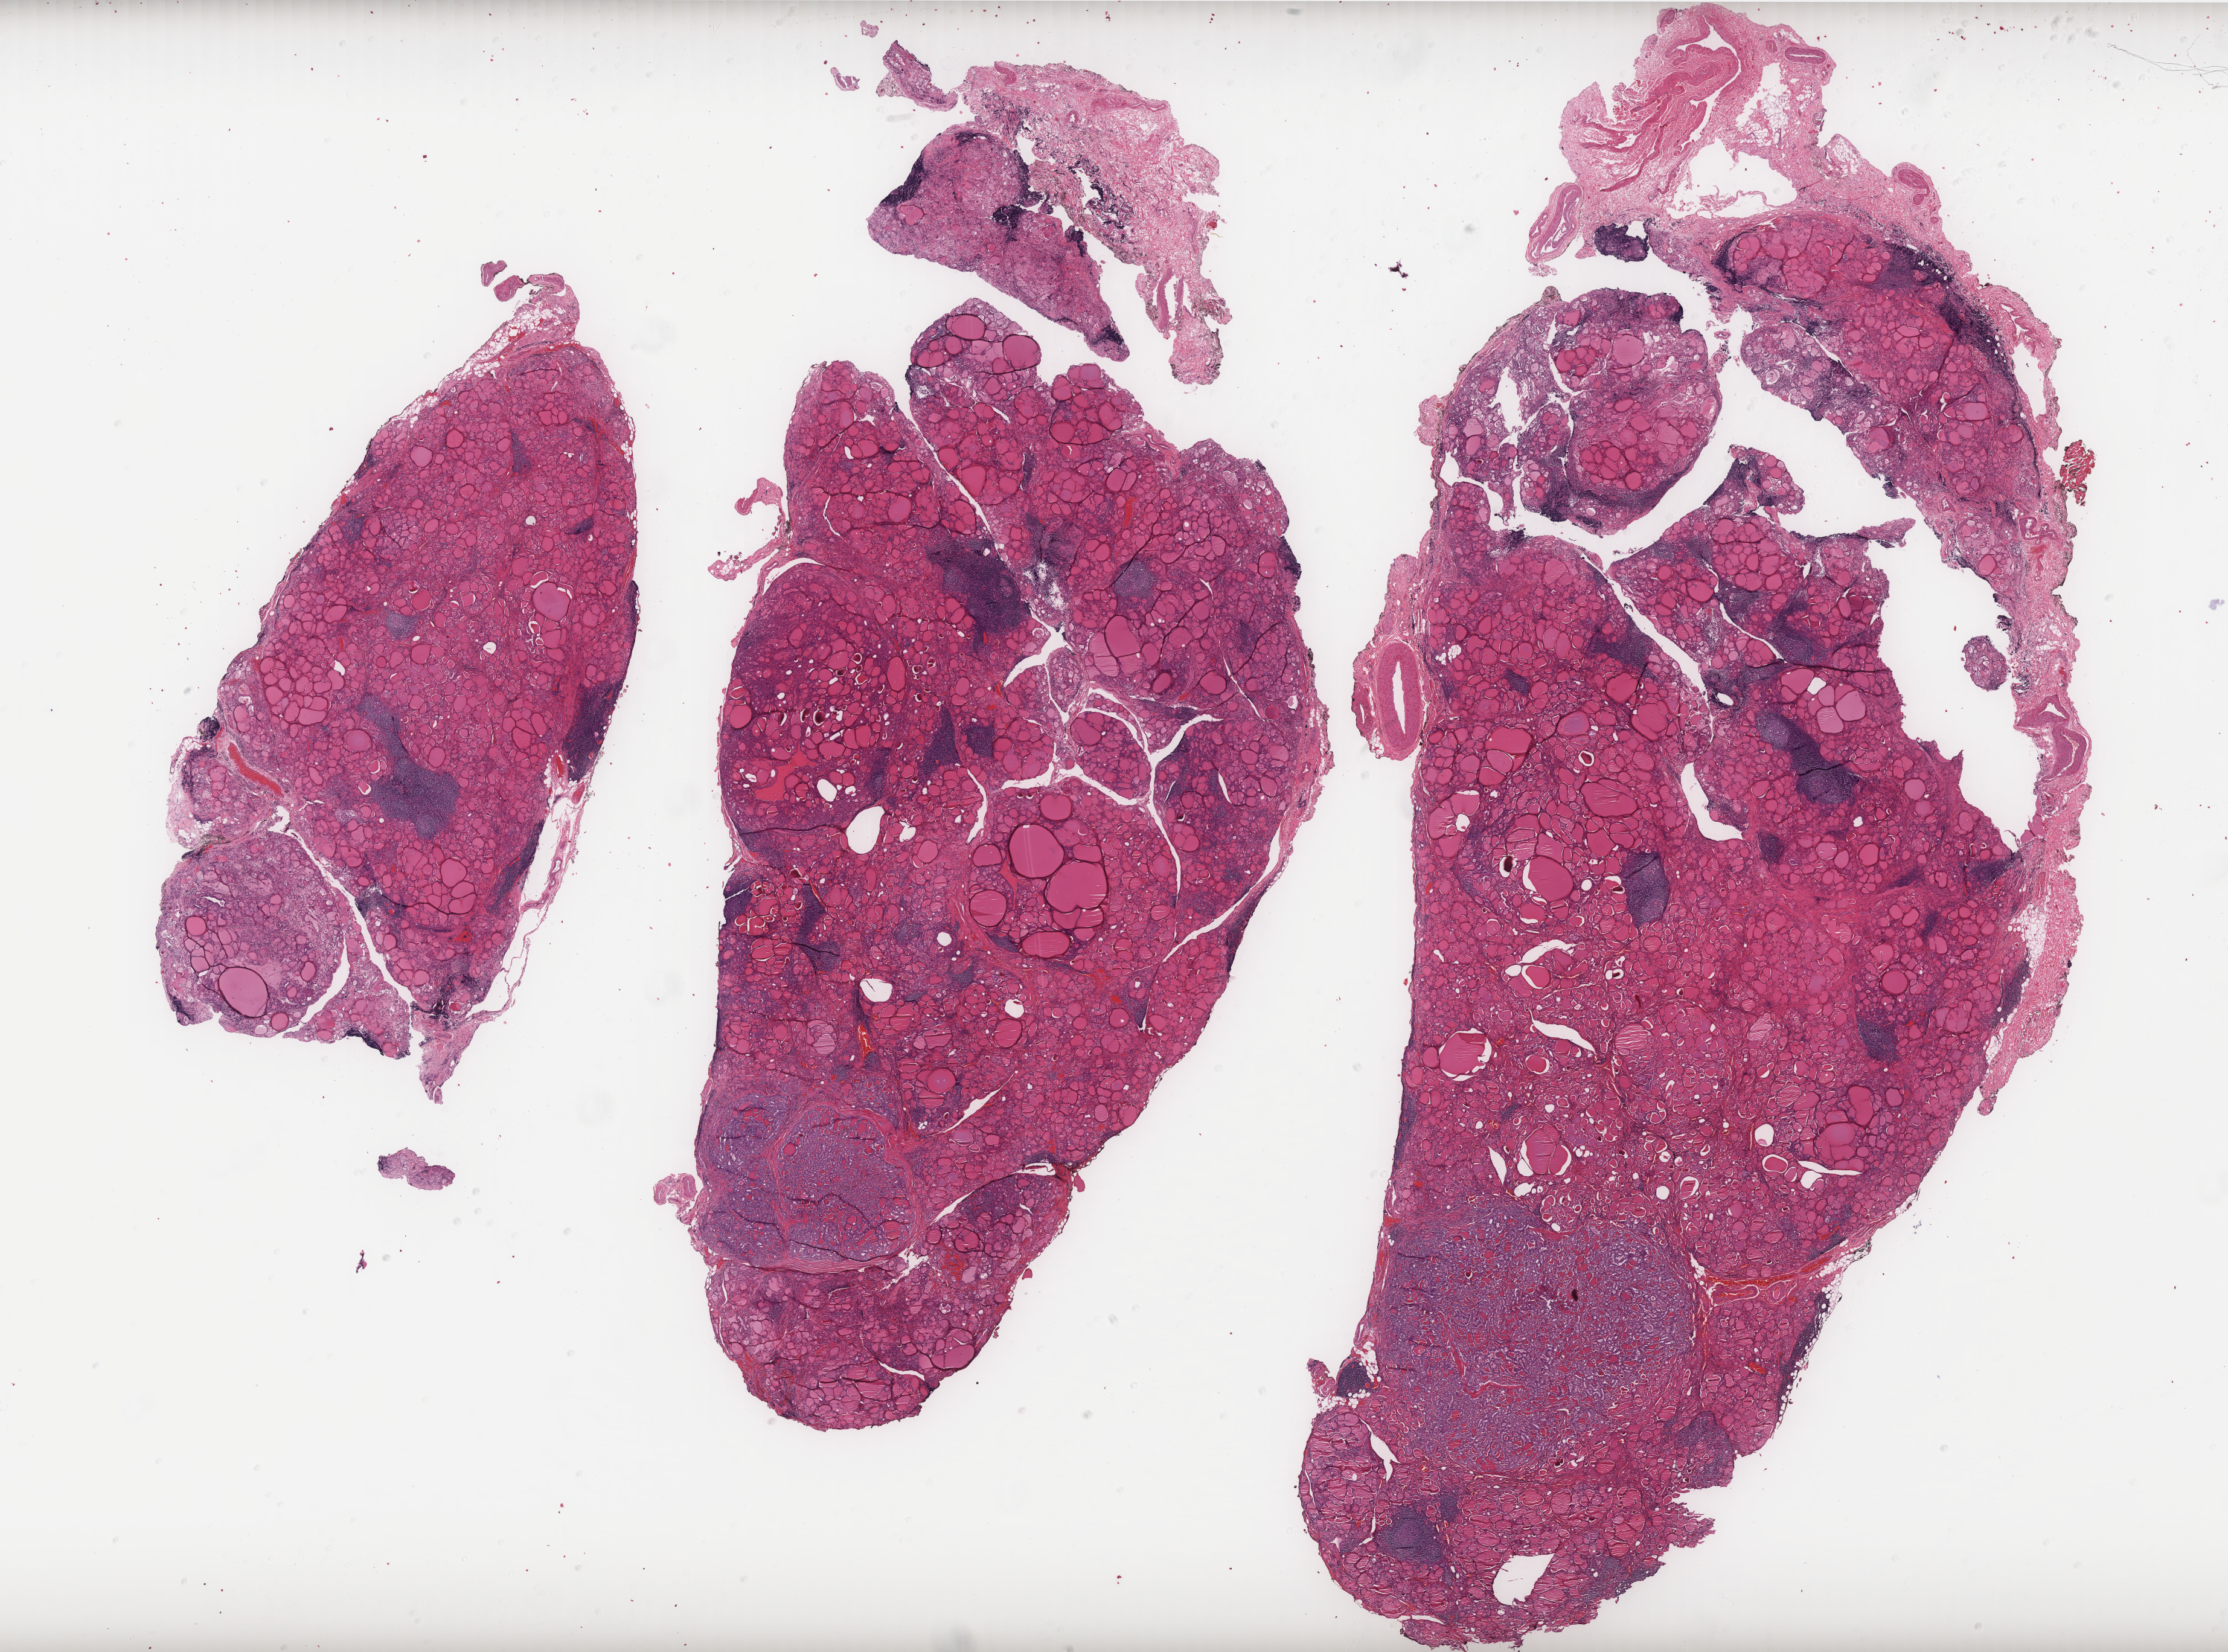
H&E-stained whole-slide image, shown as a low-resolution overview of the whole scanned area (about 29.6 x 21.9 mm, slide scanned at 40x); formalin-fixed paraffin-embedded (FFPE) diagnostic section; sample: primary tumour, thyroid. Male, age 55 years at initial diagnosis.
AJCC pathologic stage: I (7th edition). Diagnosis: Papillary adenocarcinoma, NOS (thyroid gland).